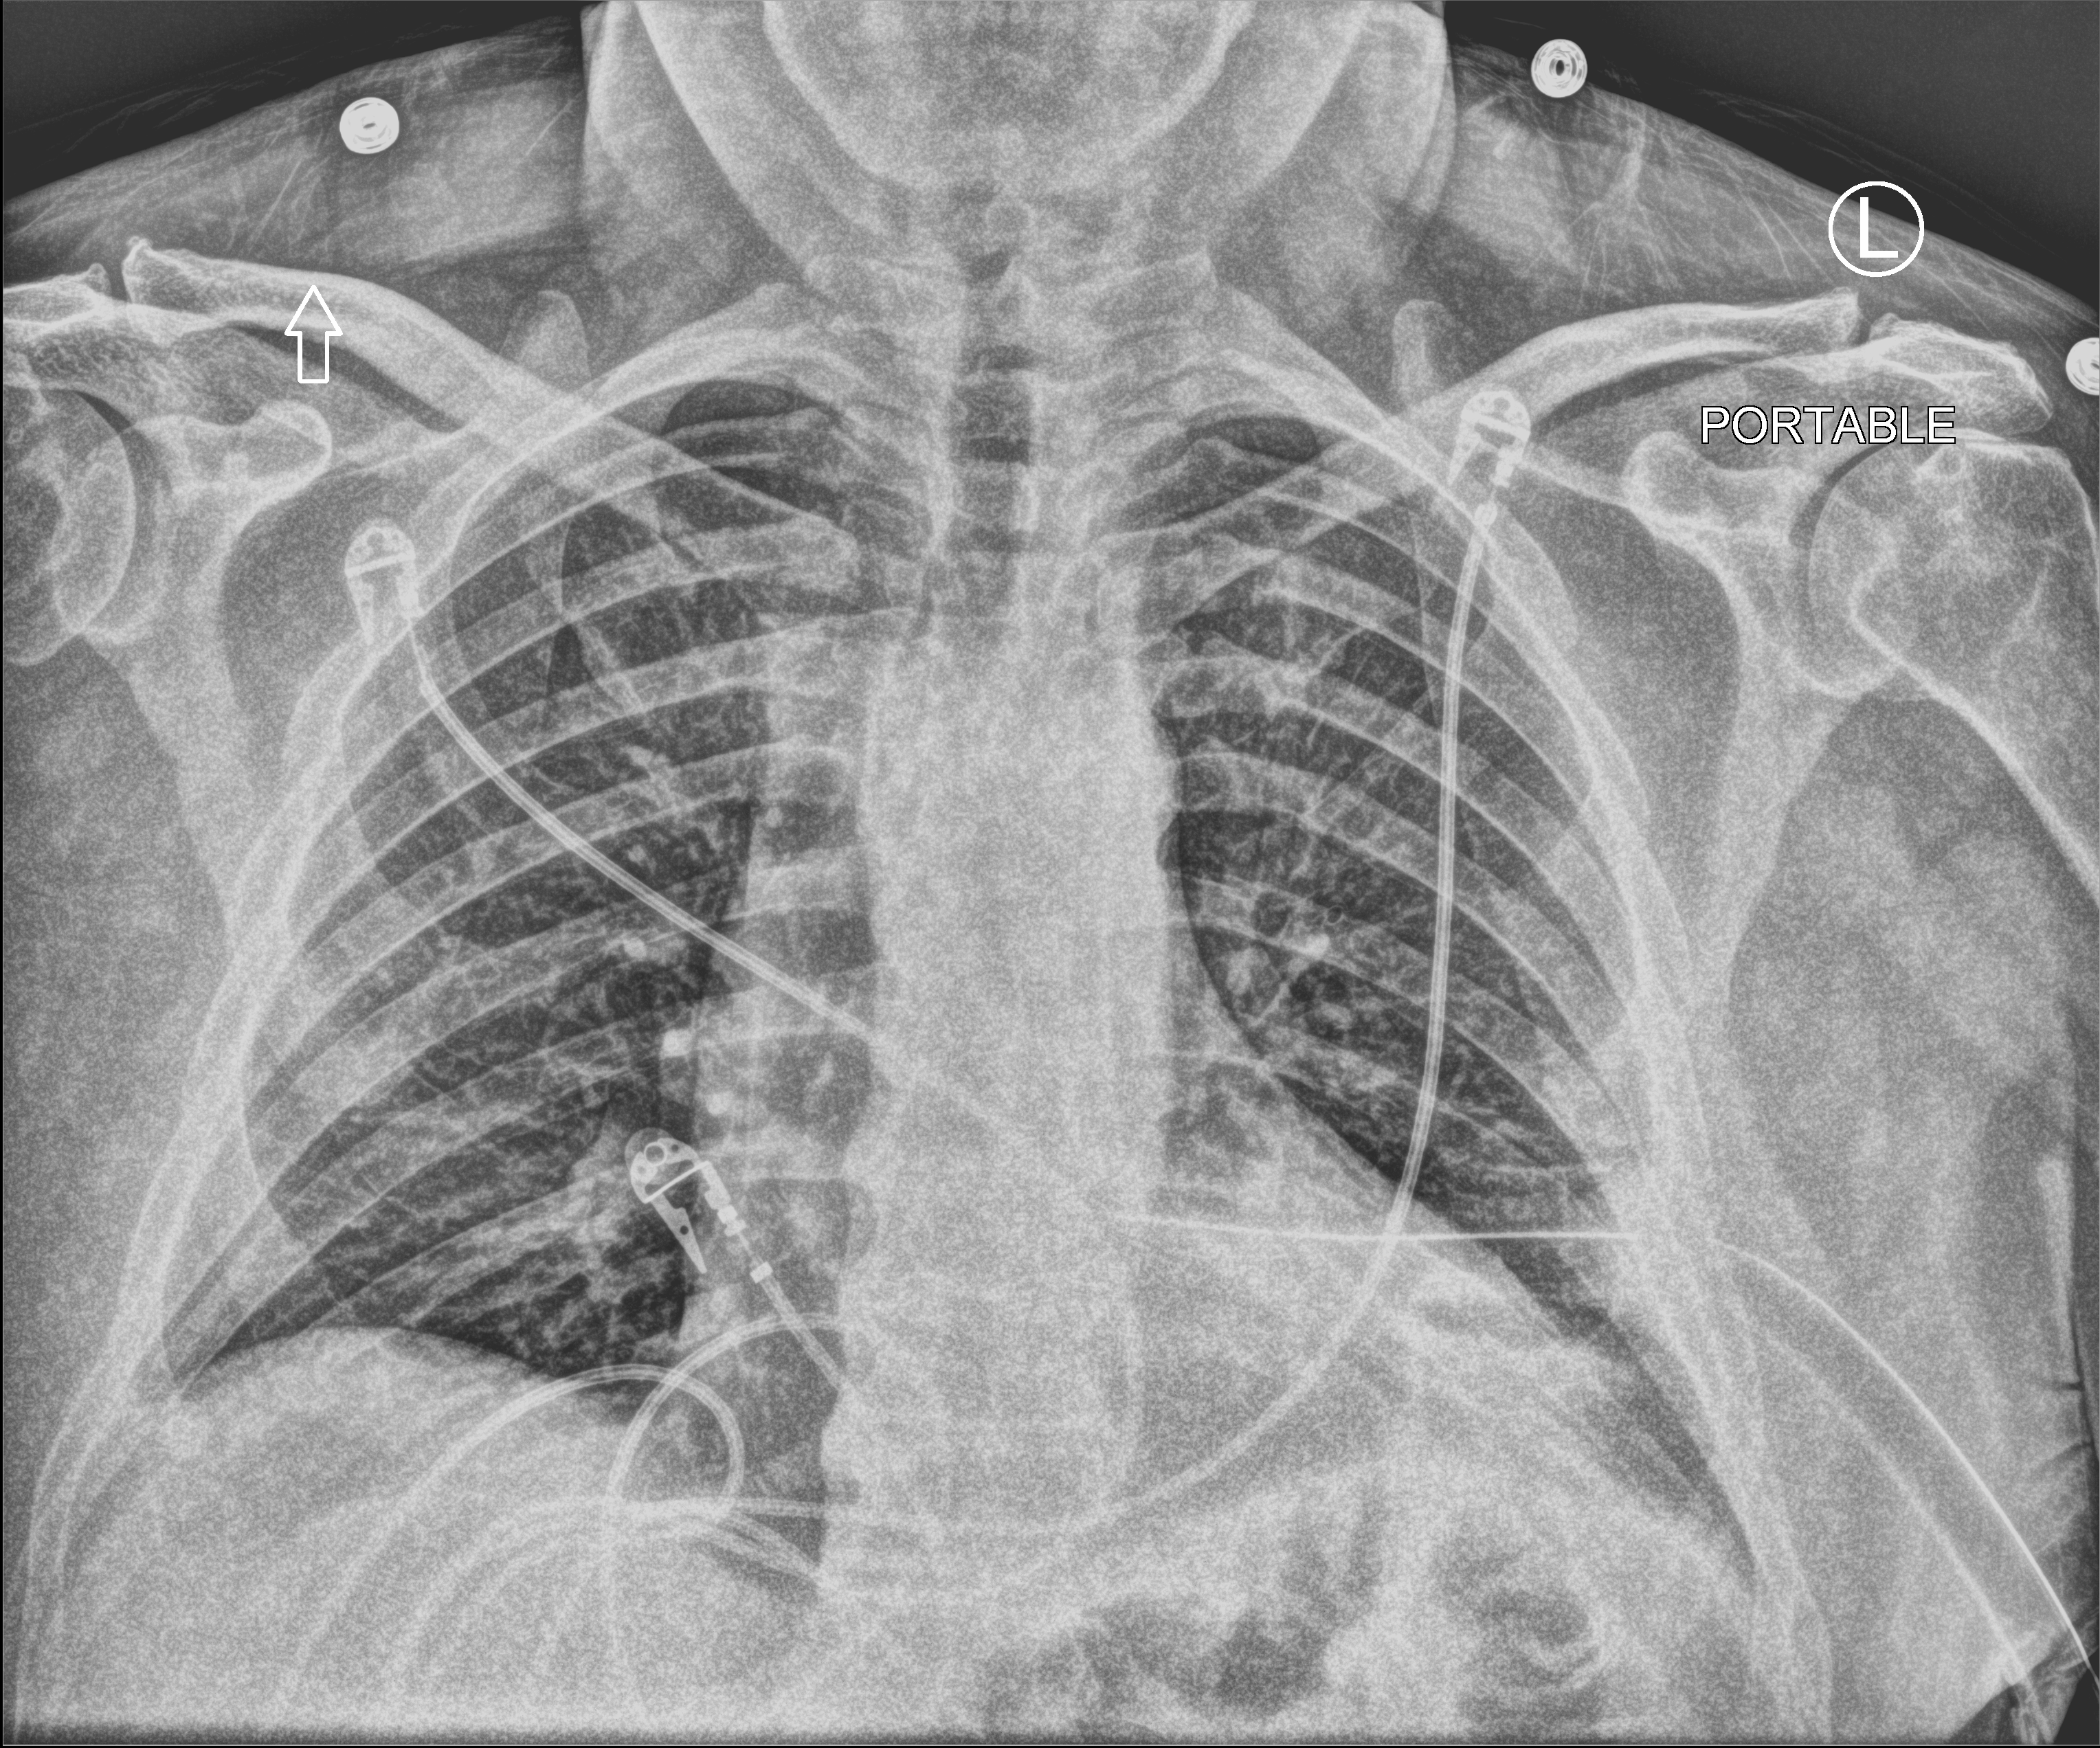
Bedside chest radiograph (computed radiography); anteroposterior (AP) projection. Male patient hospitalised with COVID-19, age 18–59 years.
From the hospital-stay record, not from the radiograph (when in the stay this image was taken is not recorded): length of hospital stay: 10 days; mechanically ventilated during this hospital stay: no; admitted to intensive care during this hospital stay: no.